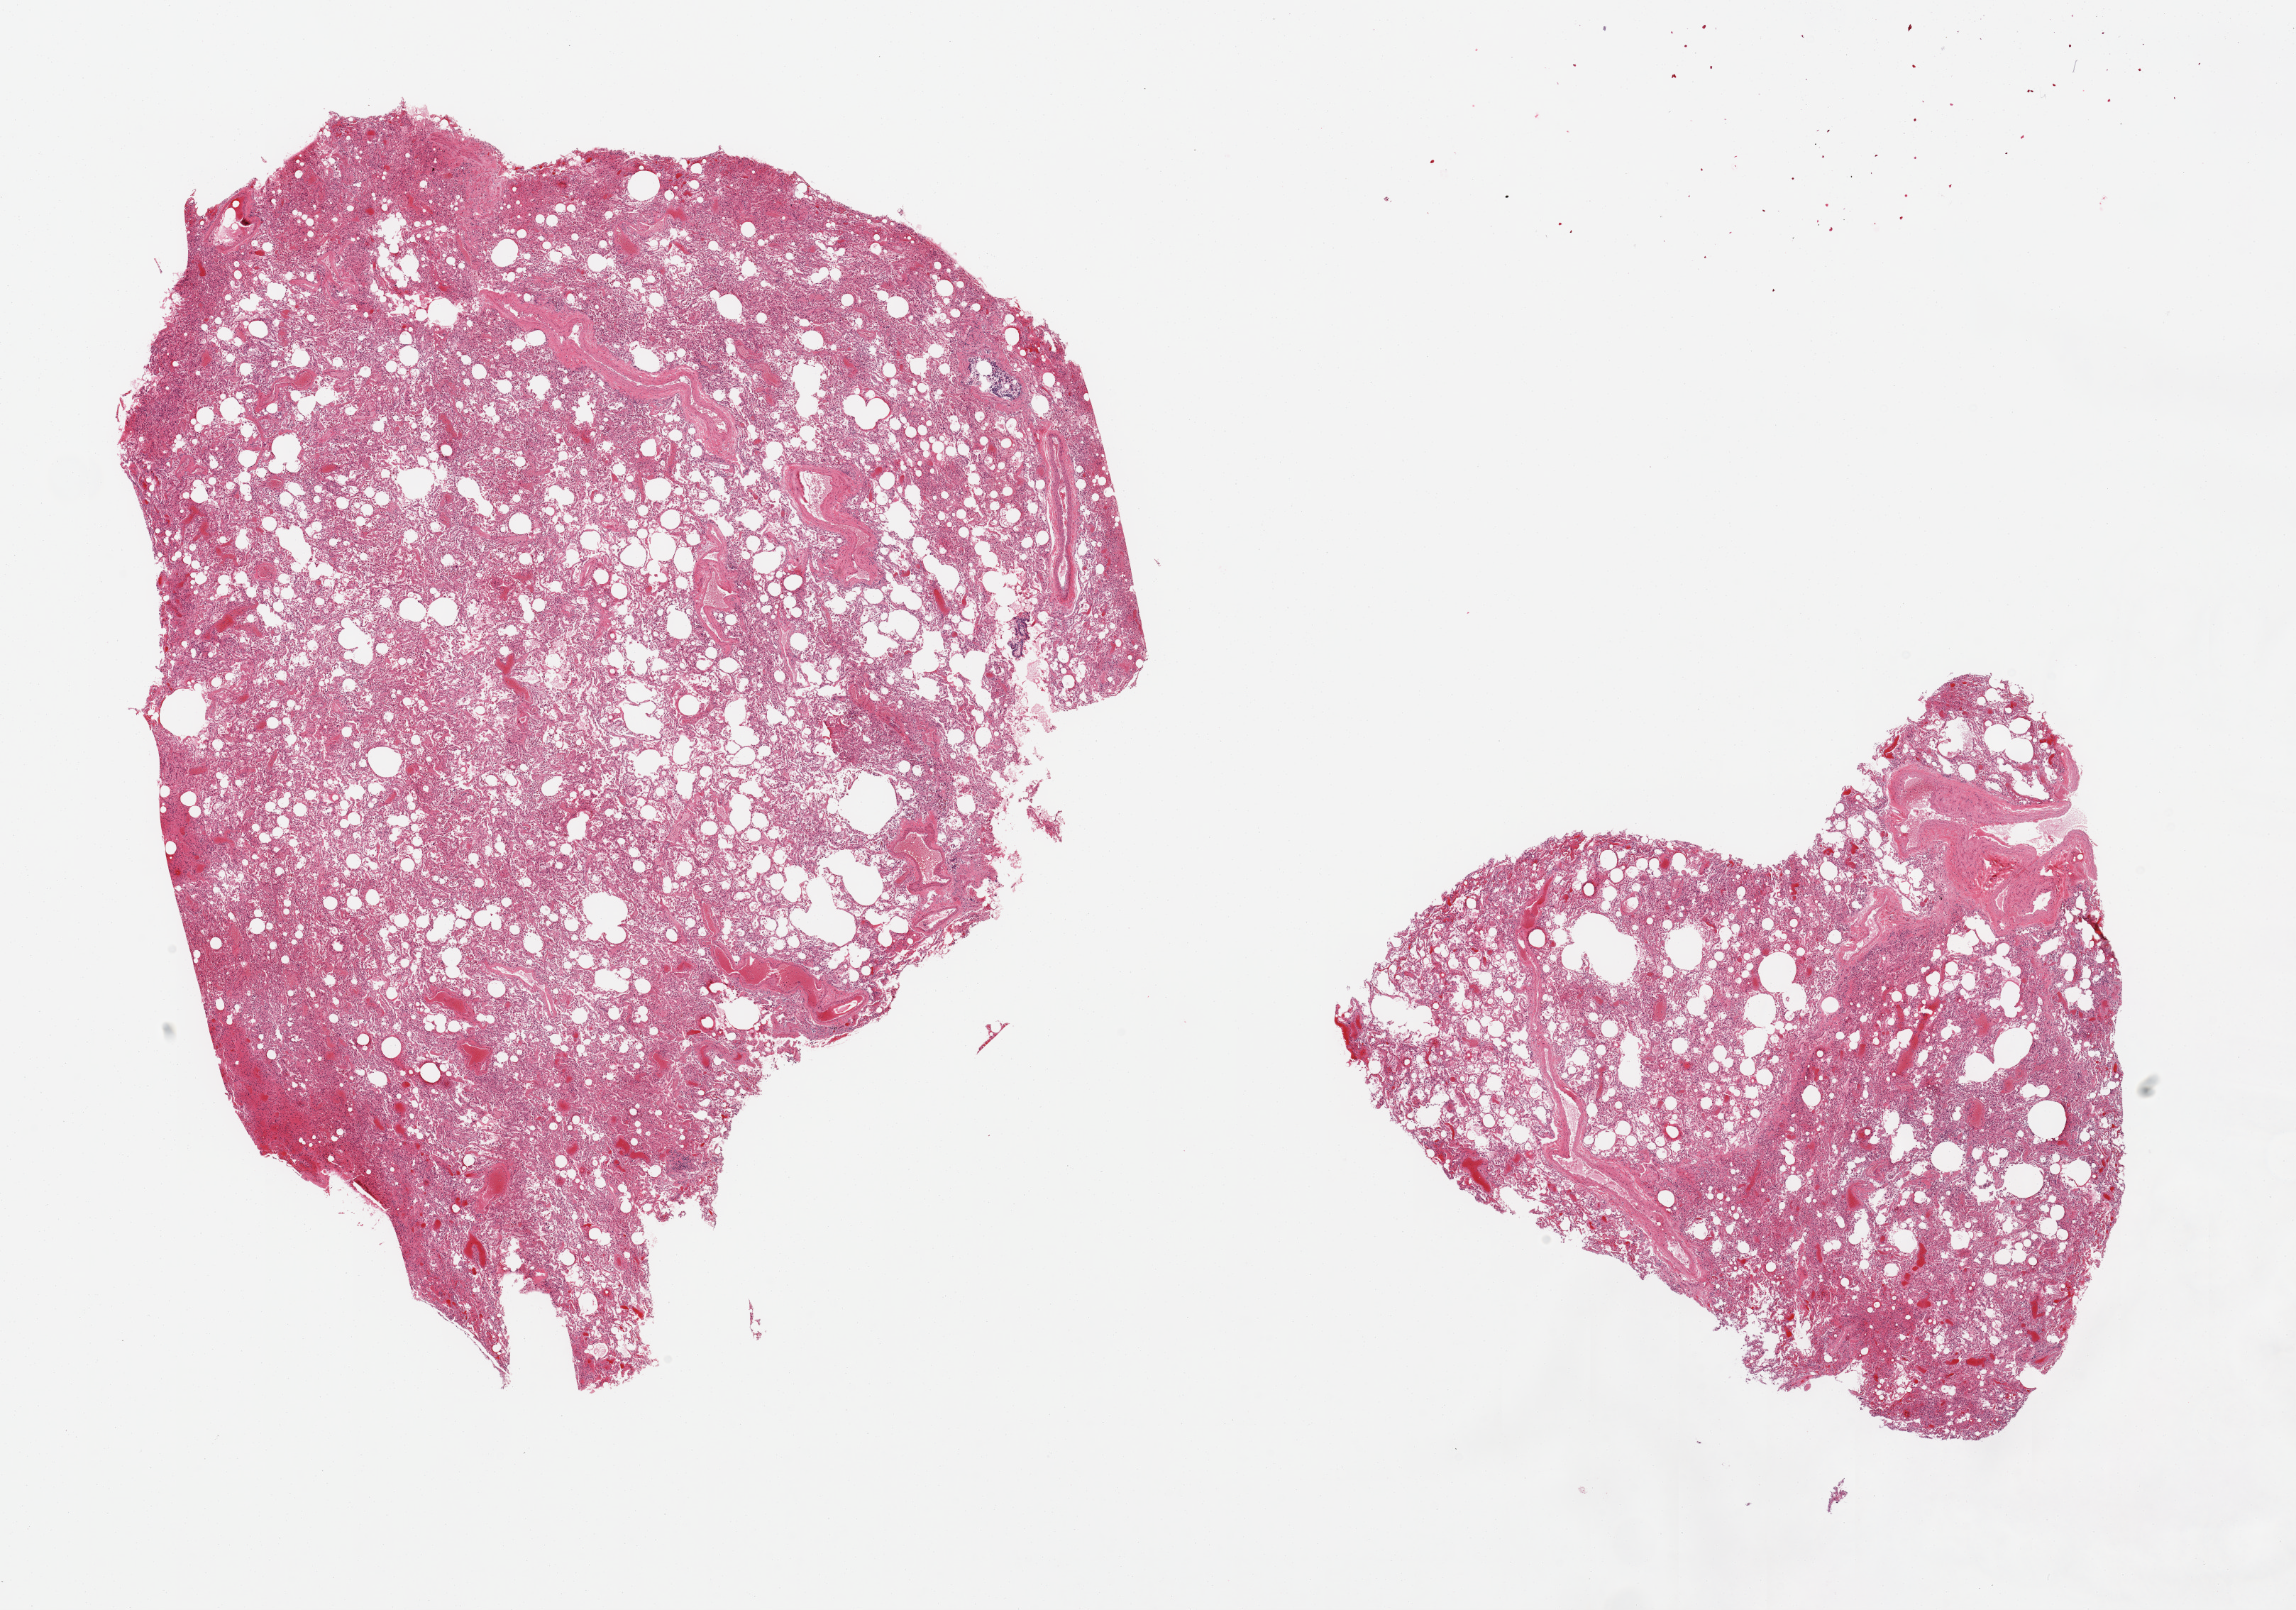
Whole-slide image, H&E stain, whole scanned area (about 25.6 x 17.9 mm) shown as a low-resolution overview; PAXgene-fixed, paraffin-embedded tissue; sampled site (target tissue): lung; tissue donor sample. Donor: male.
Reviewer comment on this tissue sample: 2 pieces; congested, emphysema, foci of hemorrhage.